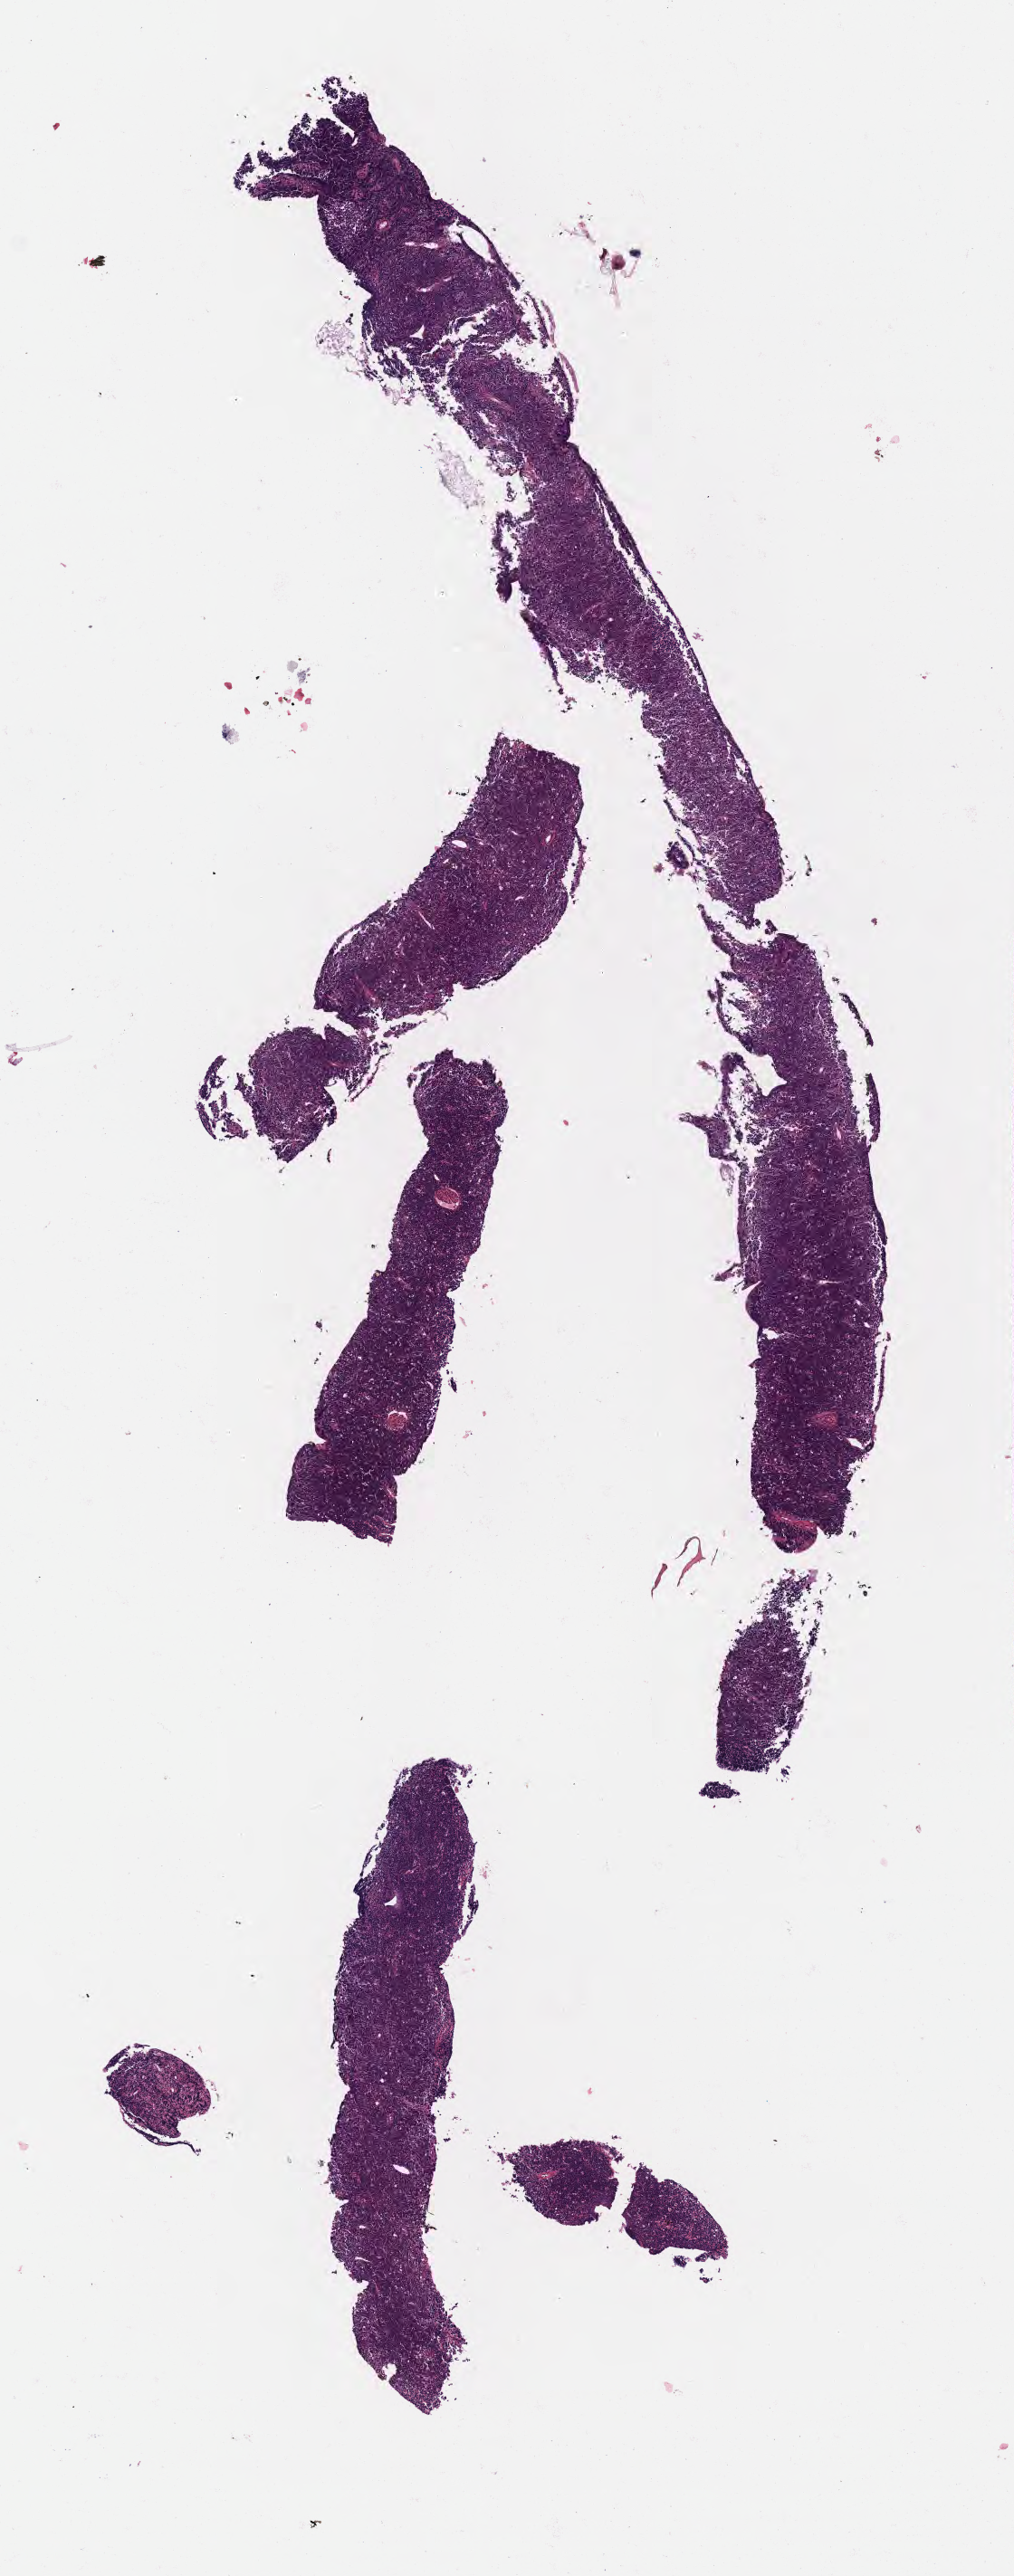
Whole-slide image, H&E stain, whole scanned area (about 4.5 x 11.5 mm) shown as a low-resolution overview, FFPE section, primary tumor. Patient: male, age at initial diagnosis 8 years. Slide review estimates, as recorded: tumor cells 95%, tumor nuclei 95%, stromal cells 5%, necrosis 0%, normal cells 0%. Infiltration values recorded for this section: lymphocyte infiltration 20%, monocyte infiltration 20%, neutrophil infiltration 5%.
- Ann Arbor stage (patient): Stage III
- diagnosis: Burkitt lymphoma, NOS